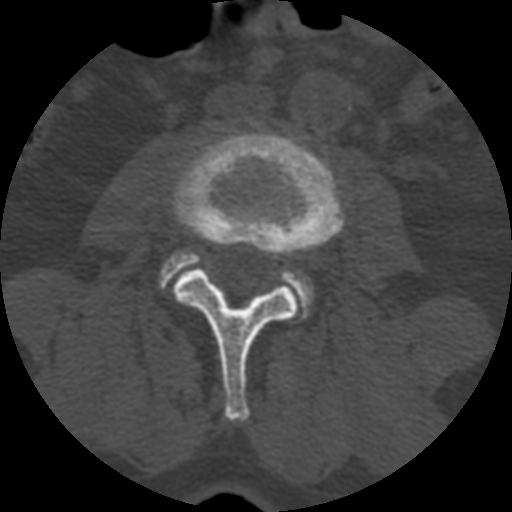
CT including the spine, one axial slice; position 299 of 399 along the scan axis; bone window (W 1800 / L 400 HU); 512 × 512 image matrix, field of view 160 × 160 mm. Patient age 71 years. Case-level facts recorded for this patient, not image findings: primary cancer: prostate.
Annotated regions visible in this slice (semi-automatically segmented with operator editing):
- L3 vertebra: bounding box [x1, y1, x2, y2] px = [172, 130, 344, 421]
- L4 vertebra: [156, 249, 313, 313]